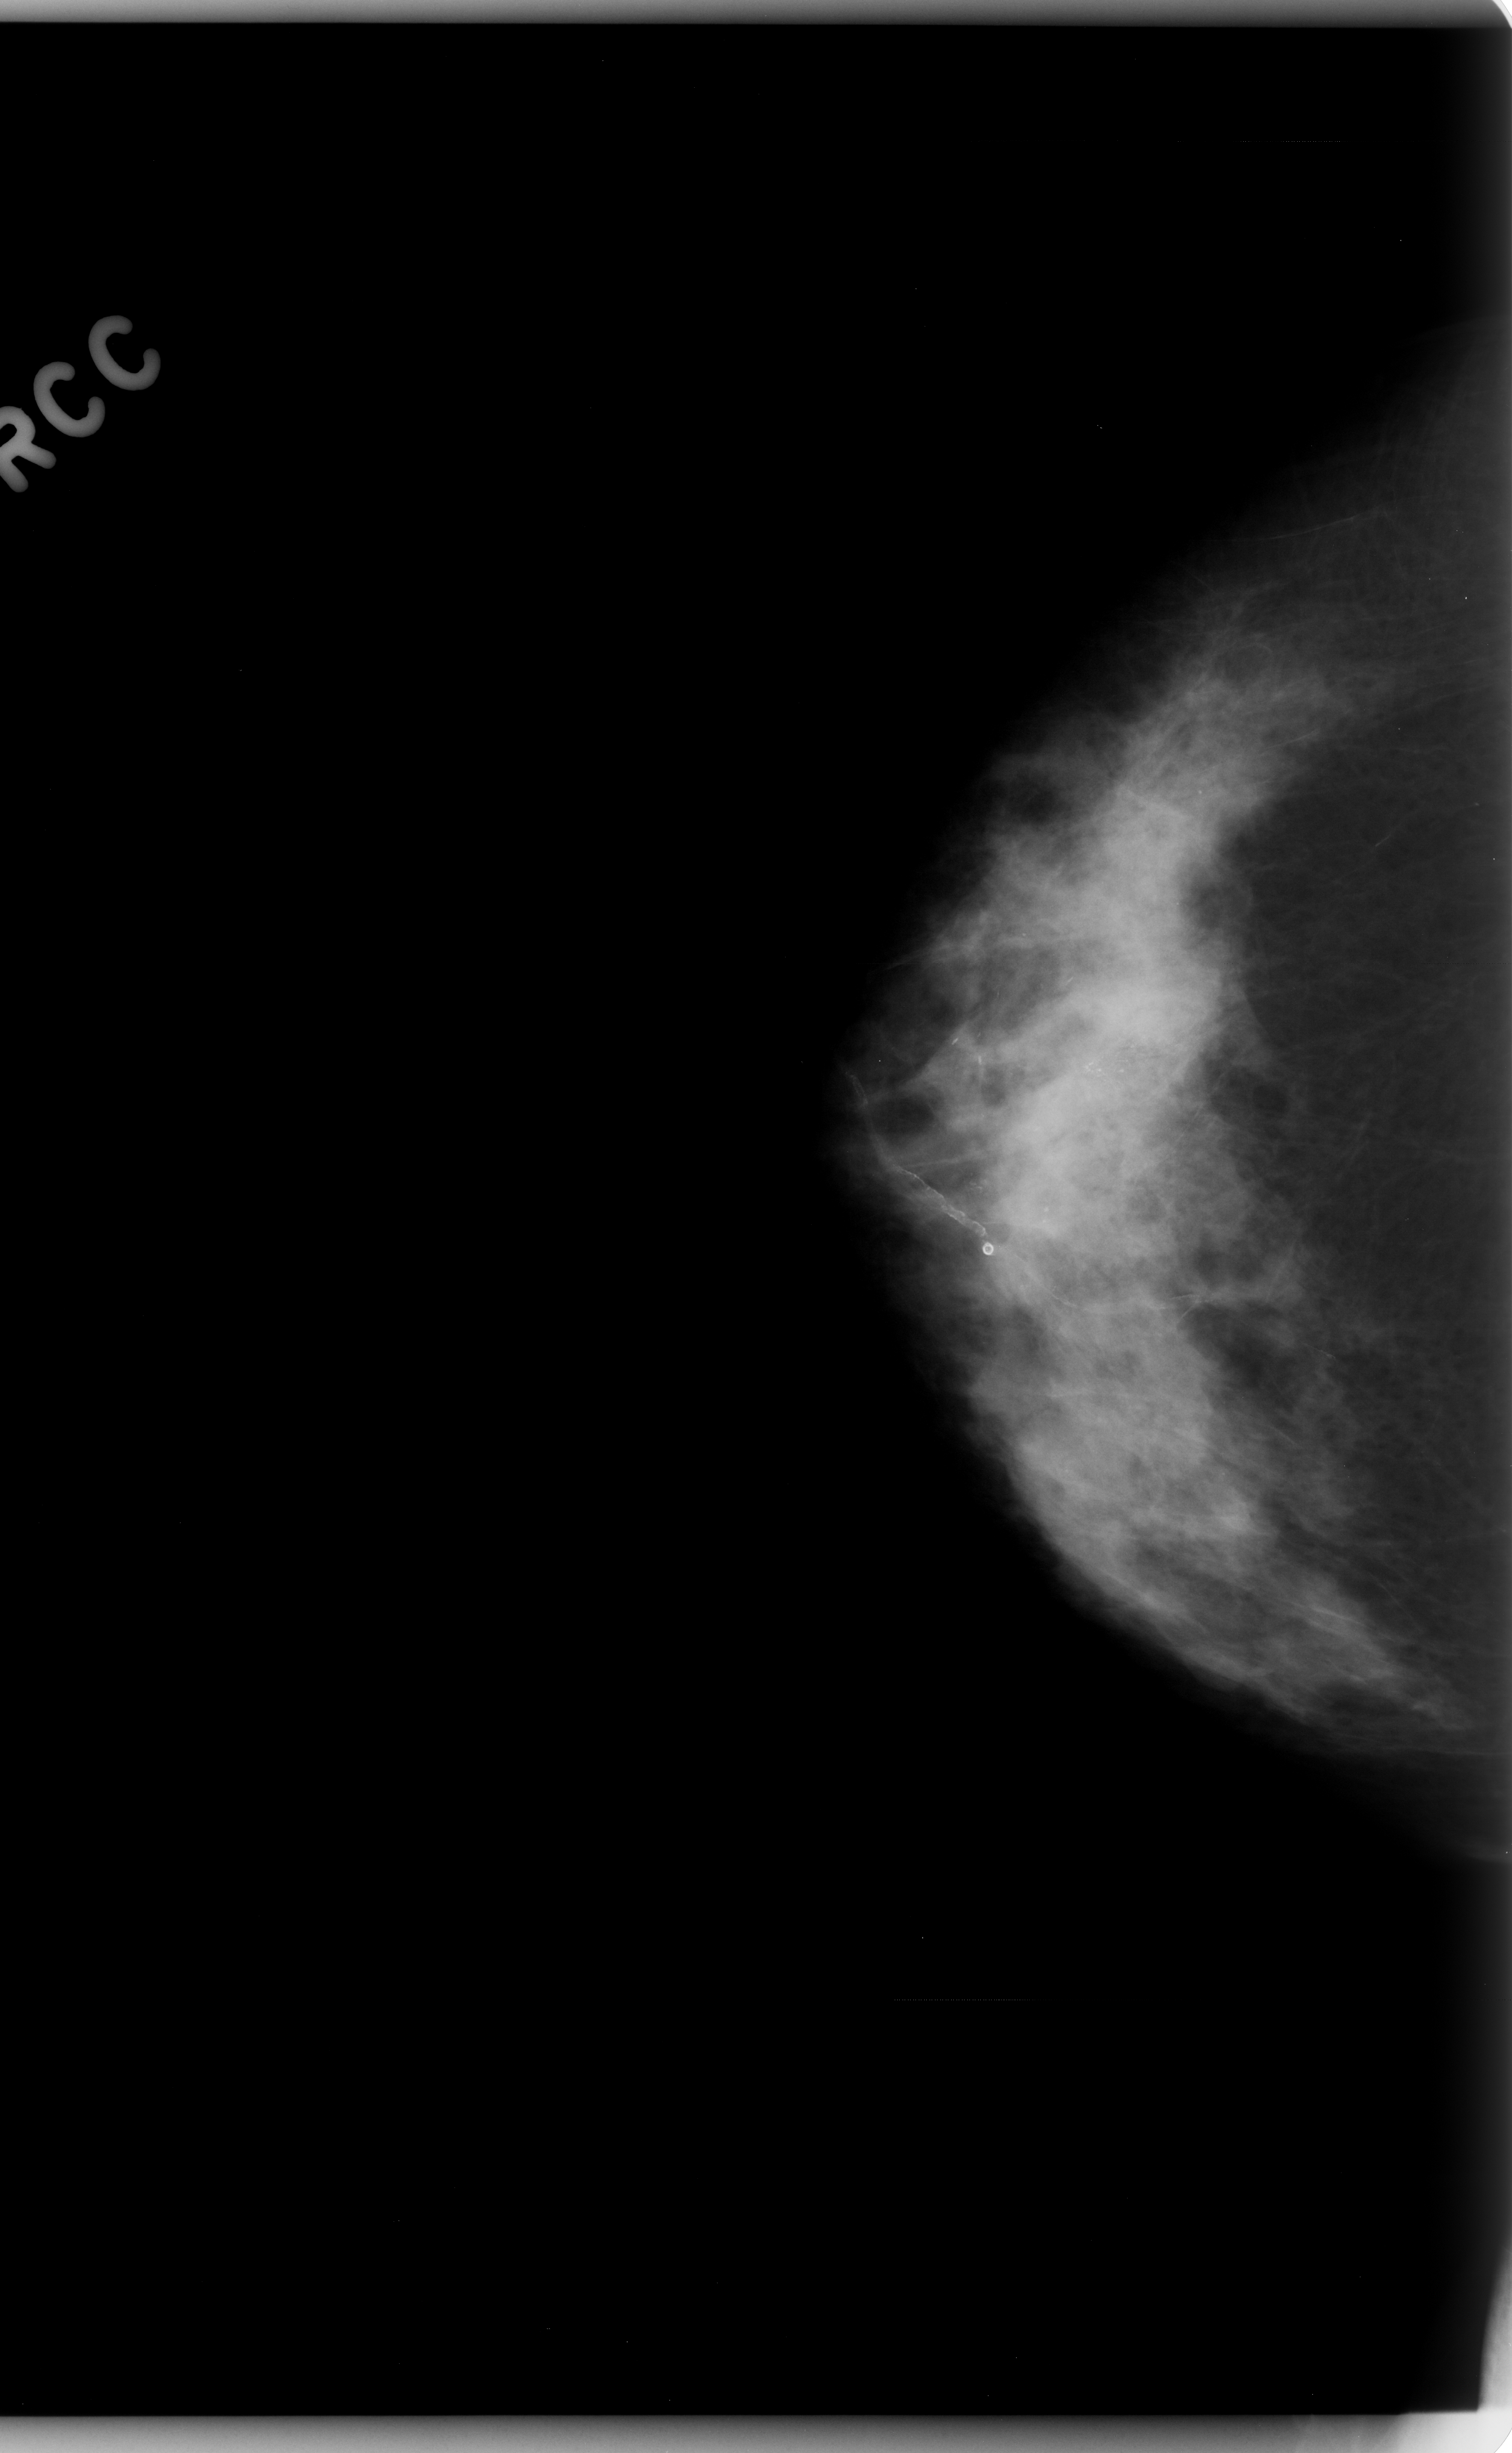
Digitized screen-film mammogram; right breast; craniocaudal (CC) view; breast composition: heterogeneously dense (BI-RADS density category 3 of 4).
- Marked findings (only marked abnormalities are described; nothing is implied about the rest of the image): calcifications, morphology fine linear branching, distribution segmental; BI-RADS assessment category 5; pathology (as recorded): malignant.